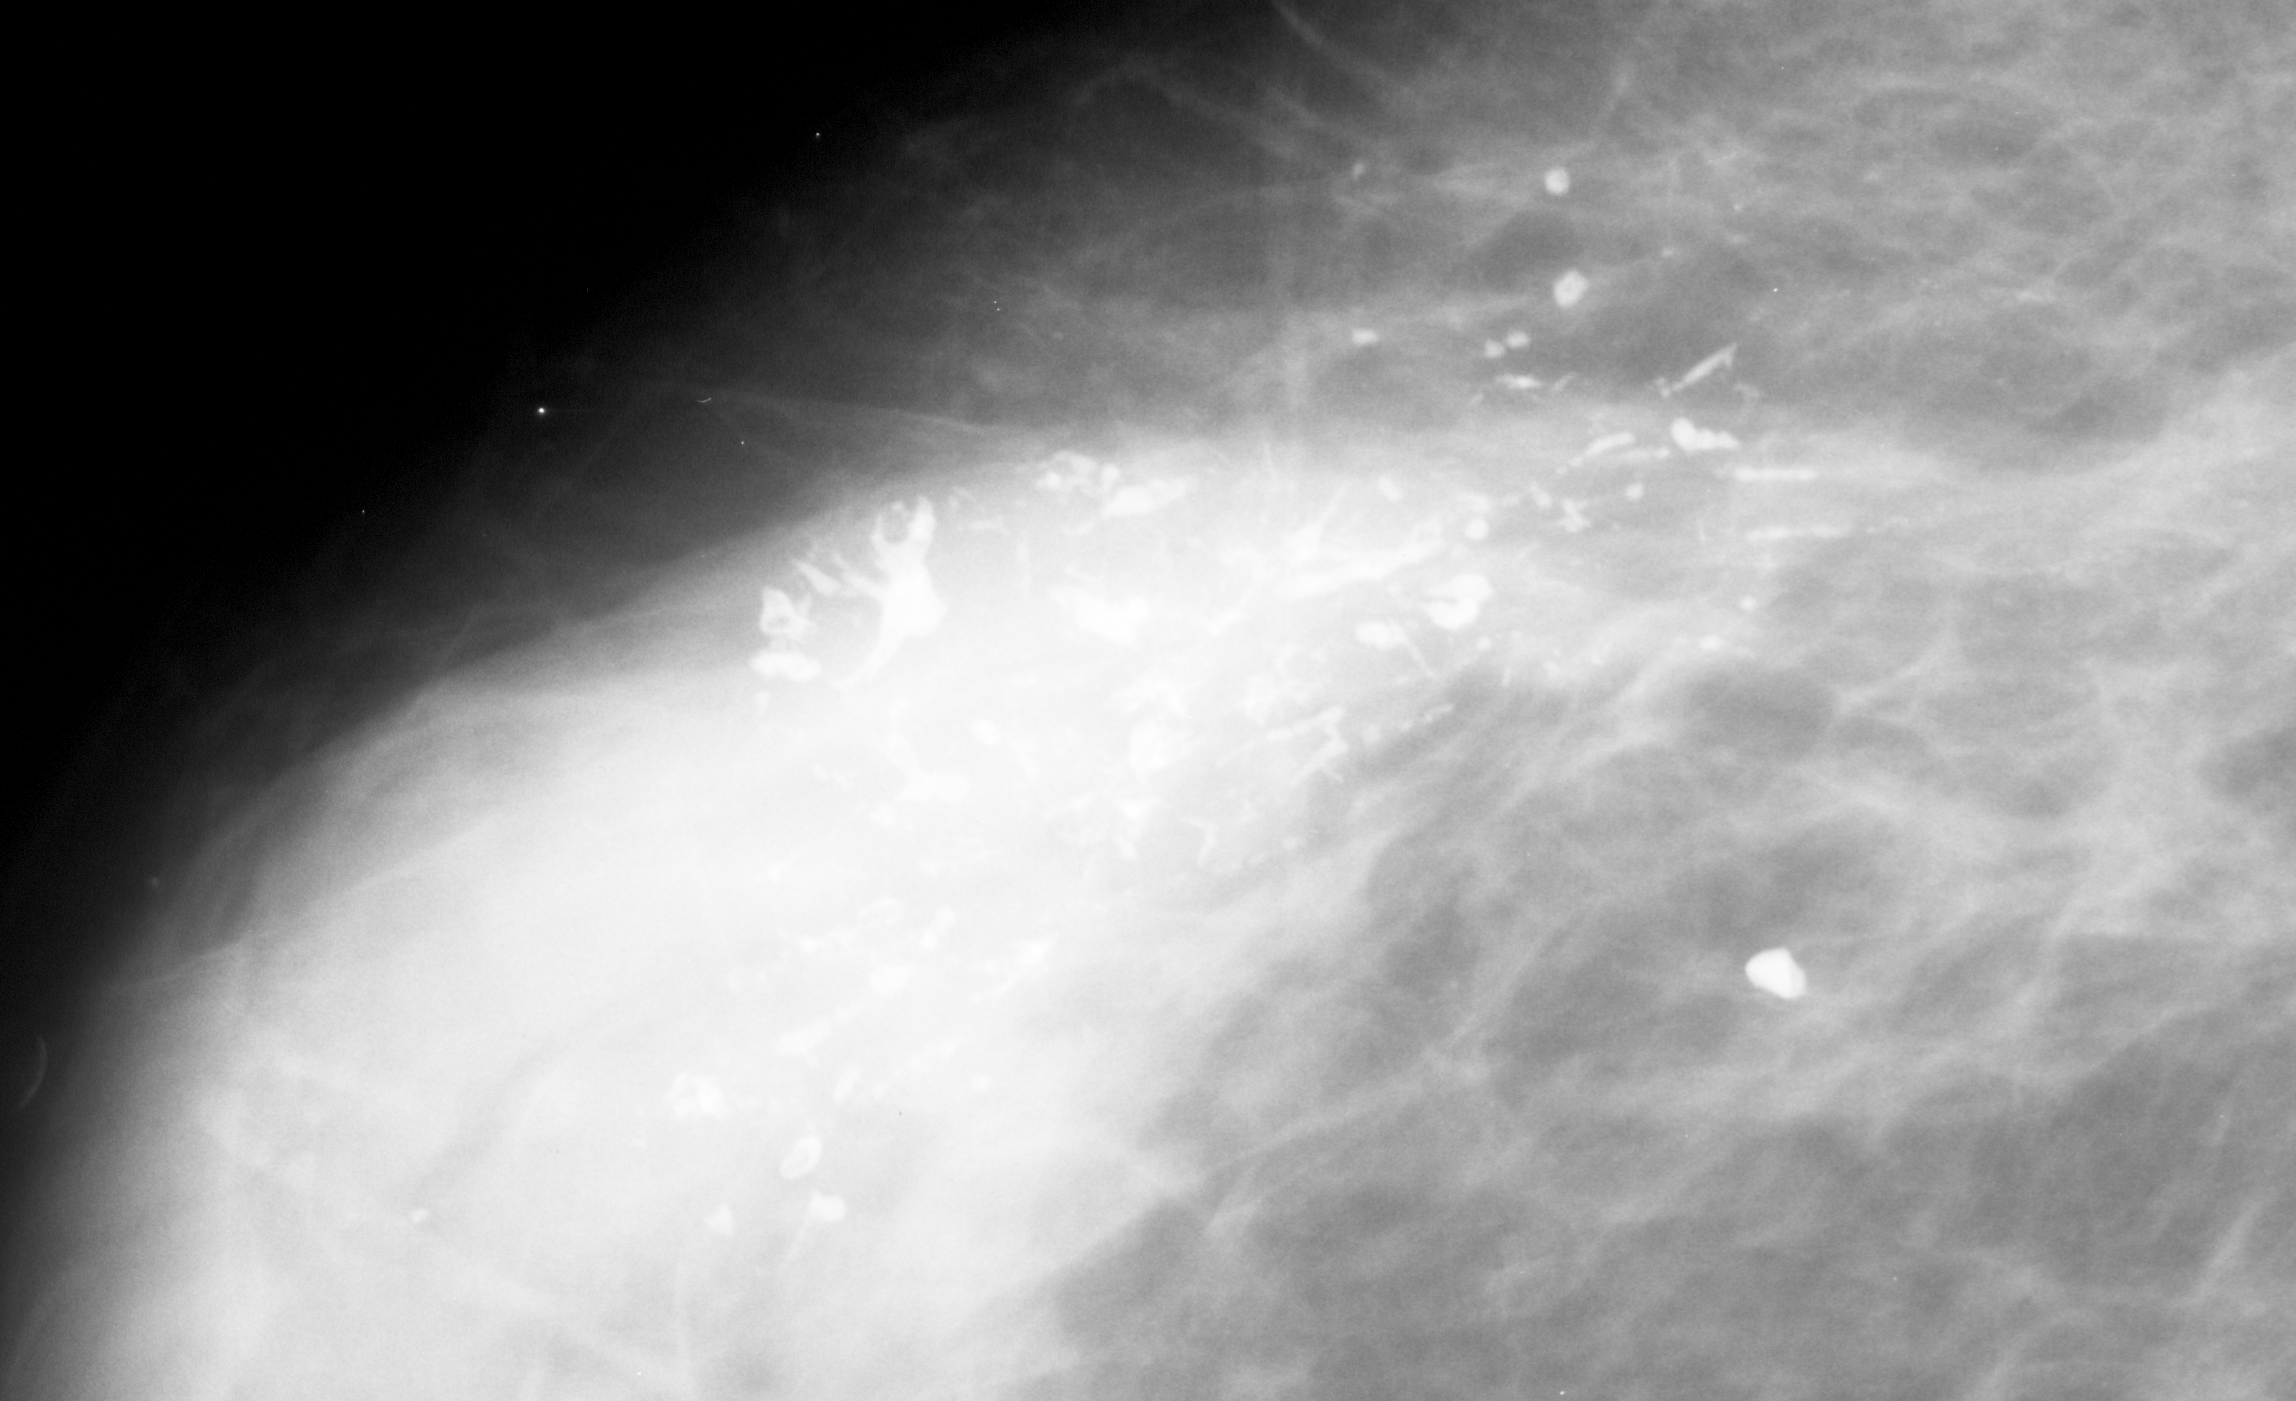
Region of interest cut from a scanned film mammogram (one marked finding); left breast; MLO view; BI-RADS breast density category 4 (scale 1–4).
- Finding: calcifications, morphology pleomorphic, distribution segmental; BI-RADS assessment category 5; subtlety rating 5 on a 1 (subtle) to 5 (obvious) scale; pathology result (as recorded, not read from the image): malignant.